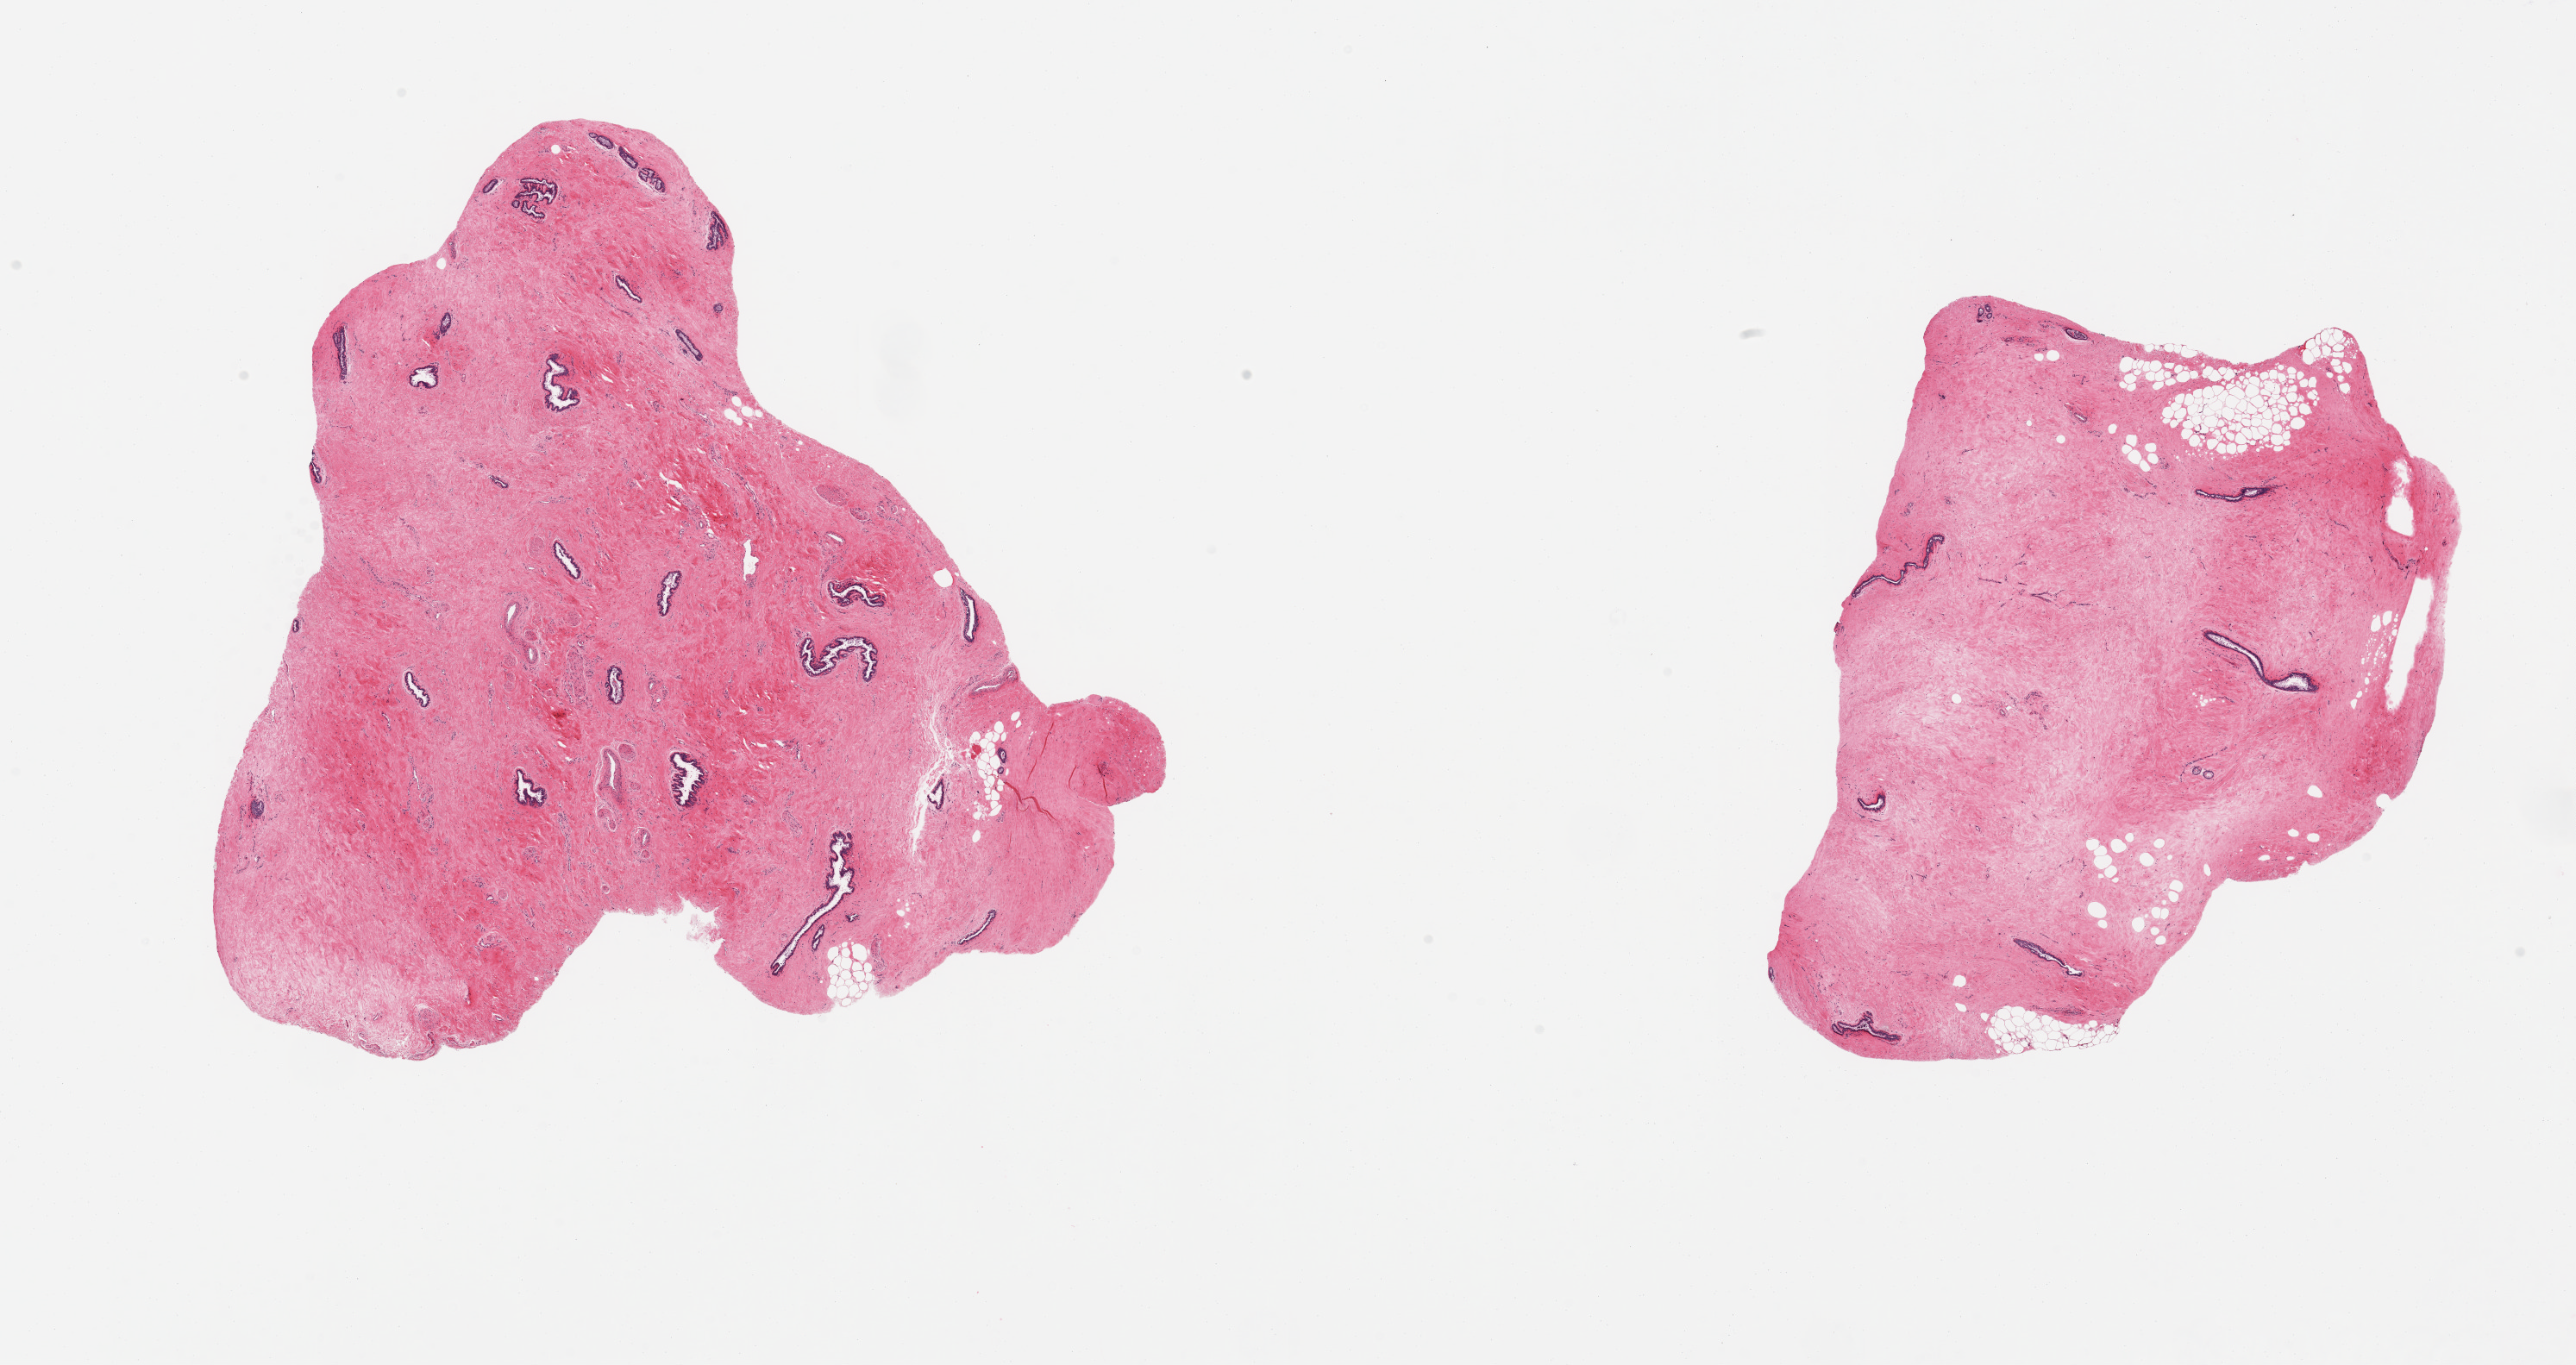
Digitized hematoxylin and eosin (H&E)-stained section — a low-resolution overview of the entire scanned area, about 23.6 x 12.5 mm (acquisition: 20x scan), PAXgene-fixed paraffin-embedded (PFPE) section, section of breast (target tissue), donor tissue sample. Donor sex: male.
Pathologist's review note for this sample: 2 pieces; gynecomastoid ductal and stromal accentuation.